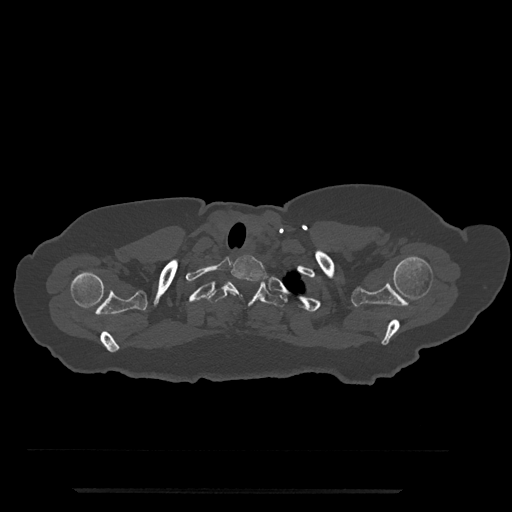
CT including the spine, one axial slice; position 689 of 797 along the scan axis; reconstruction kernel Br40s/3; 120 kVp; bone window (W 1800 / L 400 HU); 0.5 mm slice thickness; 512 × 512 image matrix, field of view 440 × 440 mm. Patient: female, 51 years. From the clinical record (not read from this slice): primary cancer: neuro; vertebrae with lytic lesions (as recorded): T8.
Annotated regions visible in this slice (semi-automatic segmentation, software-assisted and operator-edited):
- T1 vertebra: bounding box <231,255,267,296> (left, top, right, bottom; pixels)
- T2 vertebra: <206,281,286,307>